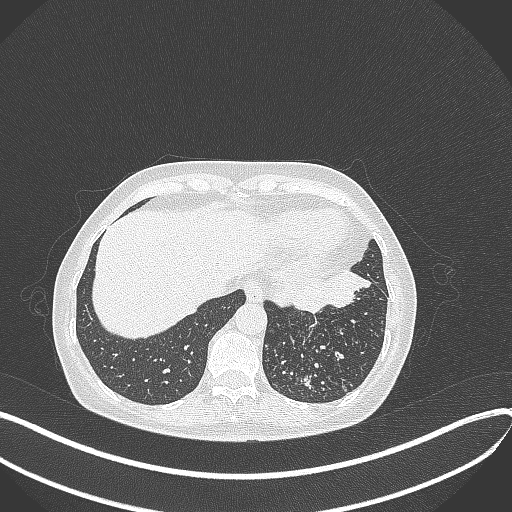
Chest CT, one axial slice. Position 90 of 429 along the scan axis. Reconstruction kernel B70f. 100 kVp. Lung window (W 1500 / L -600 HU). 512 × 512 image matrix. Female patient, age 63 years. Case-level facts recorded for this patient, not image findings: clinical TNM (as recorded): T1b N0 M0.
Annotated regions visible in this slice (bounding box drawn by a radiologist):
- lung tumour (recorded histology: adenocarcinoma): bounding box <277,265,369,308> (left, top, right, bottom; pixels)